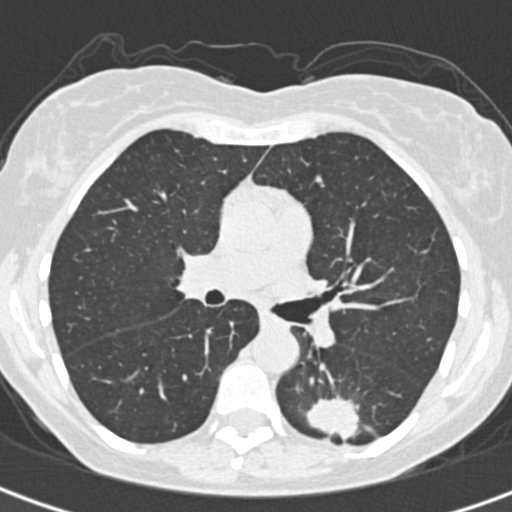
Low-dose screening chest CT, one axial slice; slice 198 of 328 in the series (ordered by position); reconstruction kernel B30f; 120 kVp; lung window (W 1500 / L -600 HU); 1 mm slice thickness; 512 × 512 image matrix.
Annotated regions visible in this slice (outlined manually by an expert reader):
- lesion 1 (tumor, lower lobe of left lung): bounding box [x1, y1, x2, y2] px = [305, 397, 359, 440]